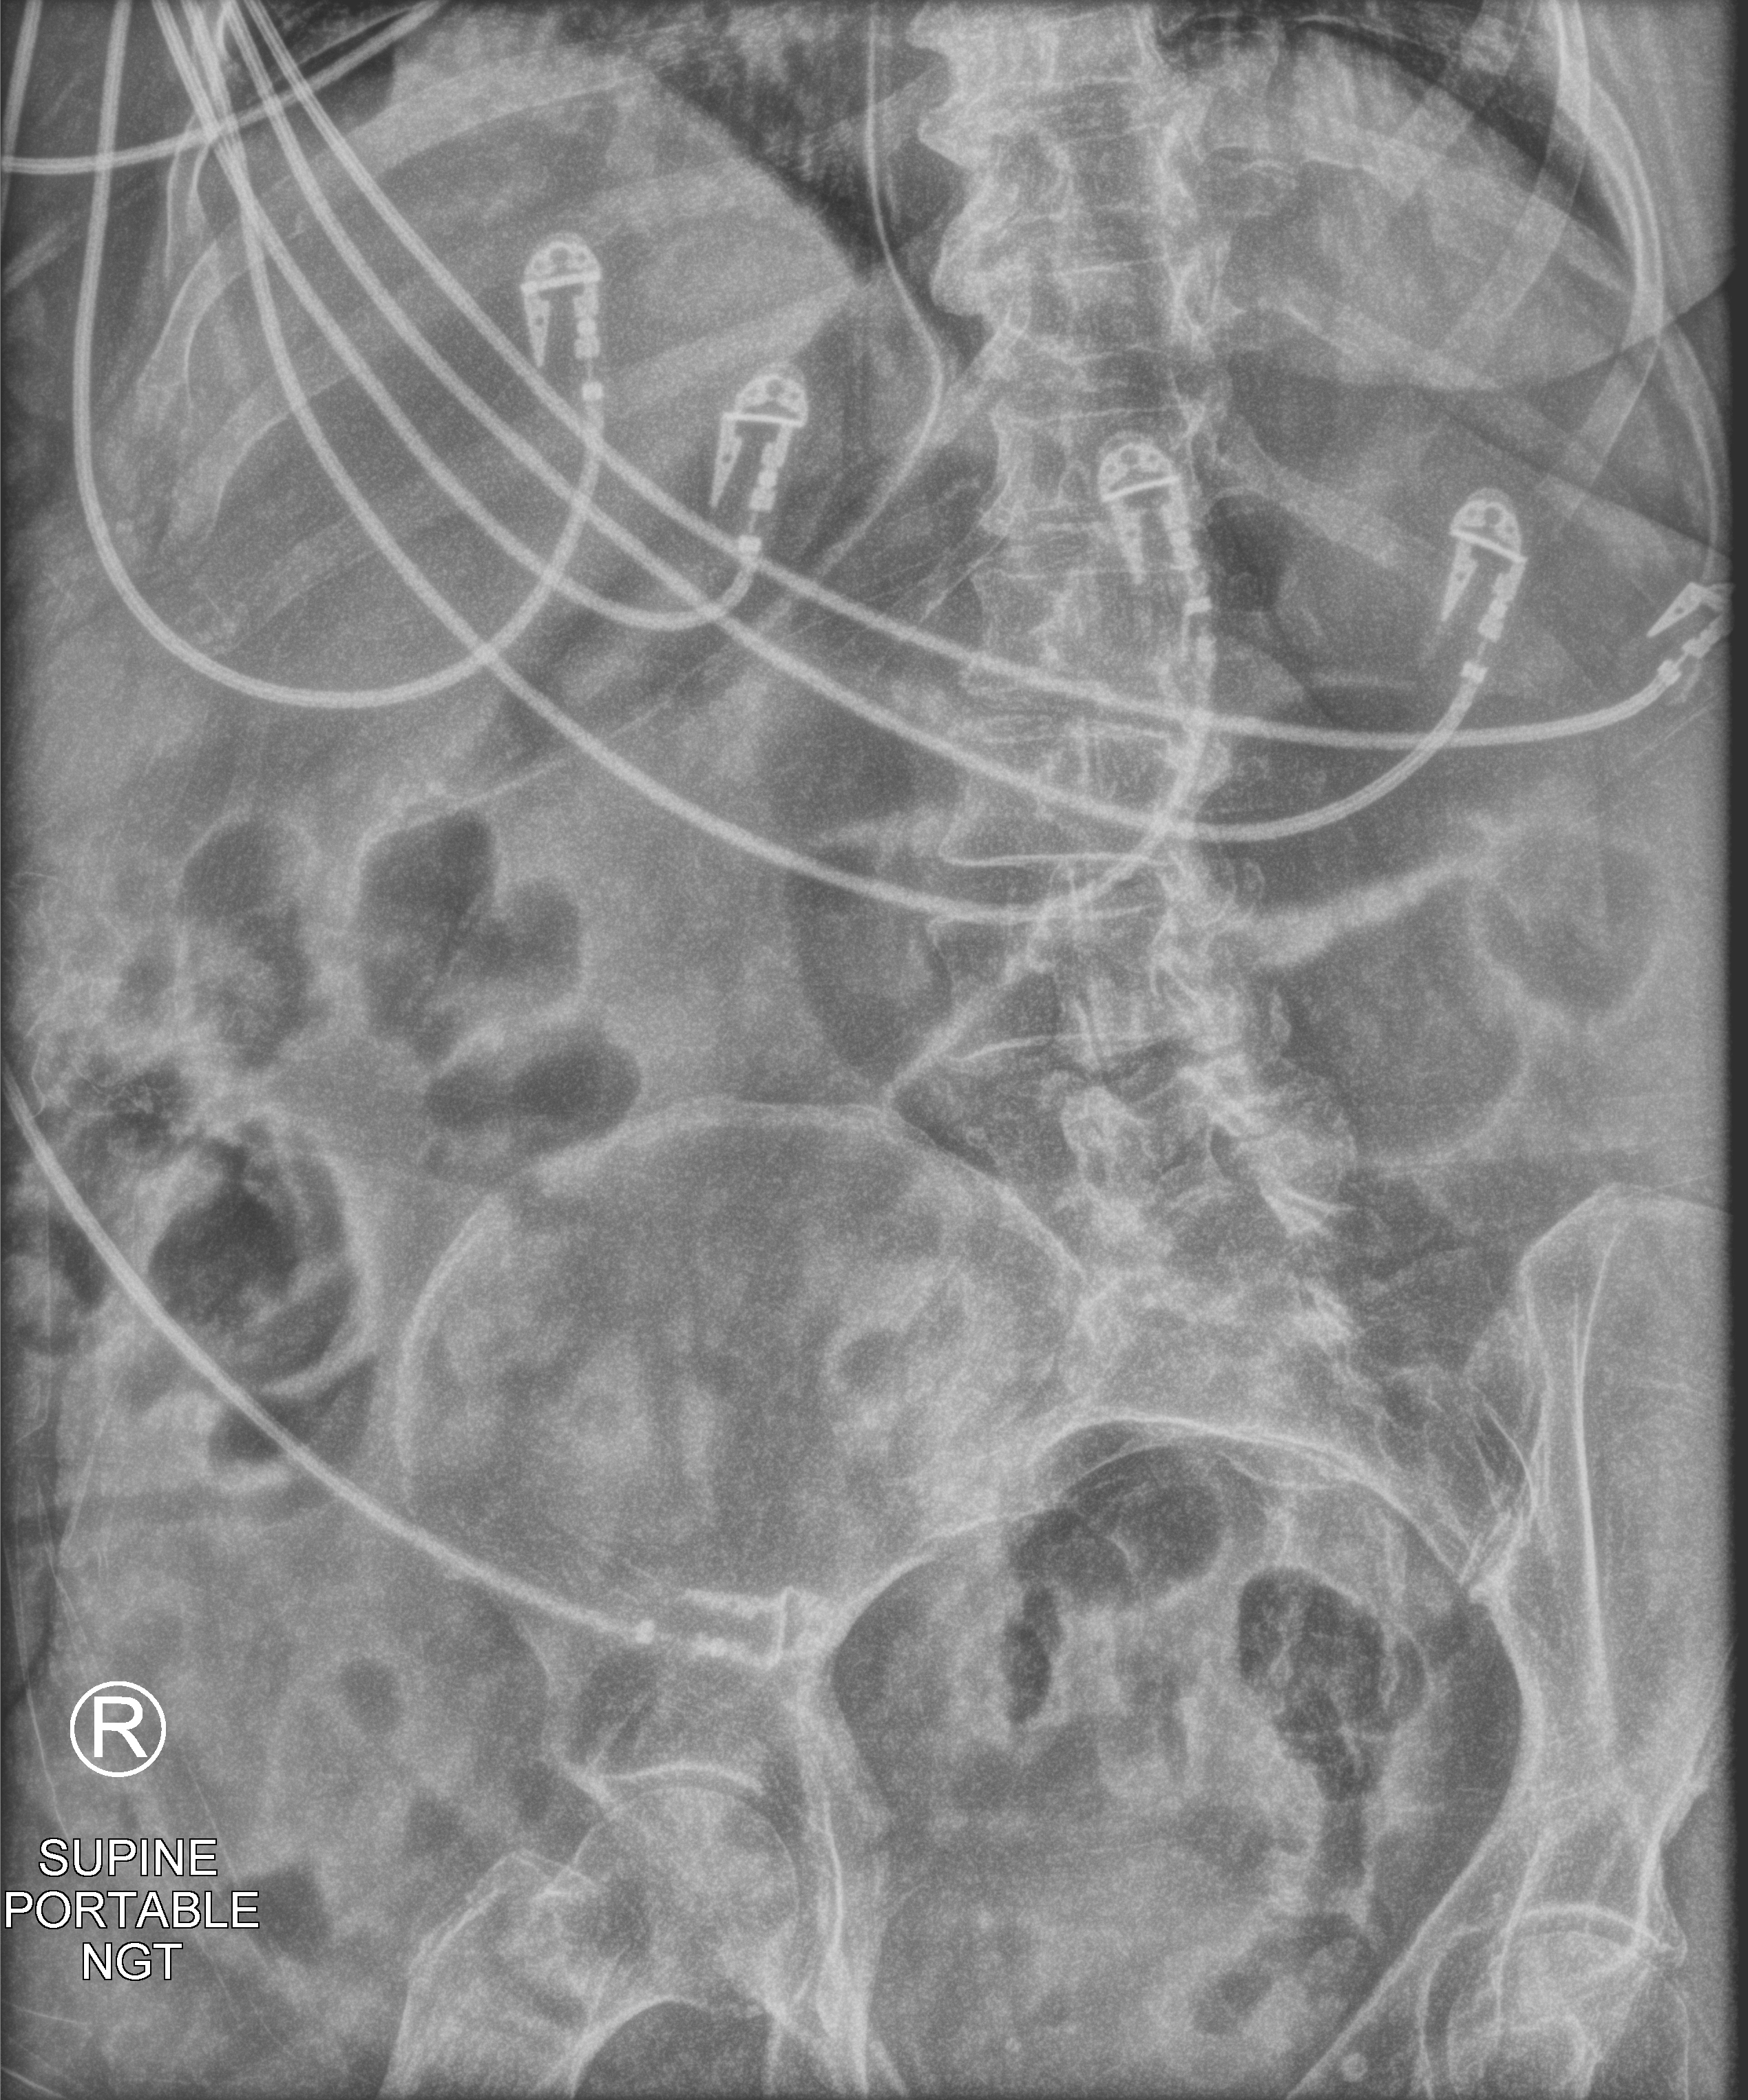
Bedside abdomen radiograph (computed radiography); anteroposterior (AP) projection. Female patient hospitalised with COVID-19, age 75–90 years.
From the hospital-stay record, not from the radiograph (when in the stay this image was taken is not recorded): hypertension (admission record): yes; admitted to intensive care during this hospital stay: yes.